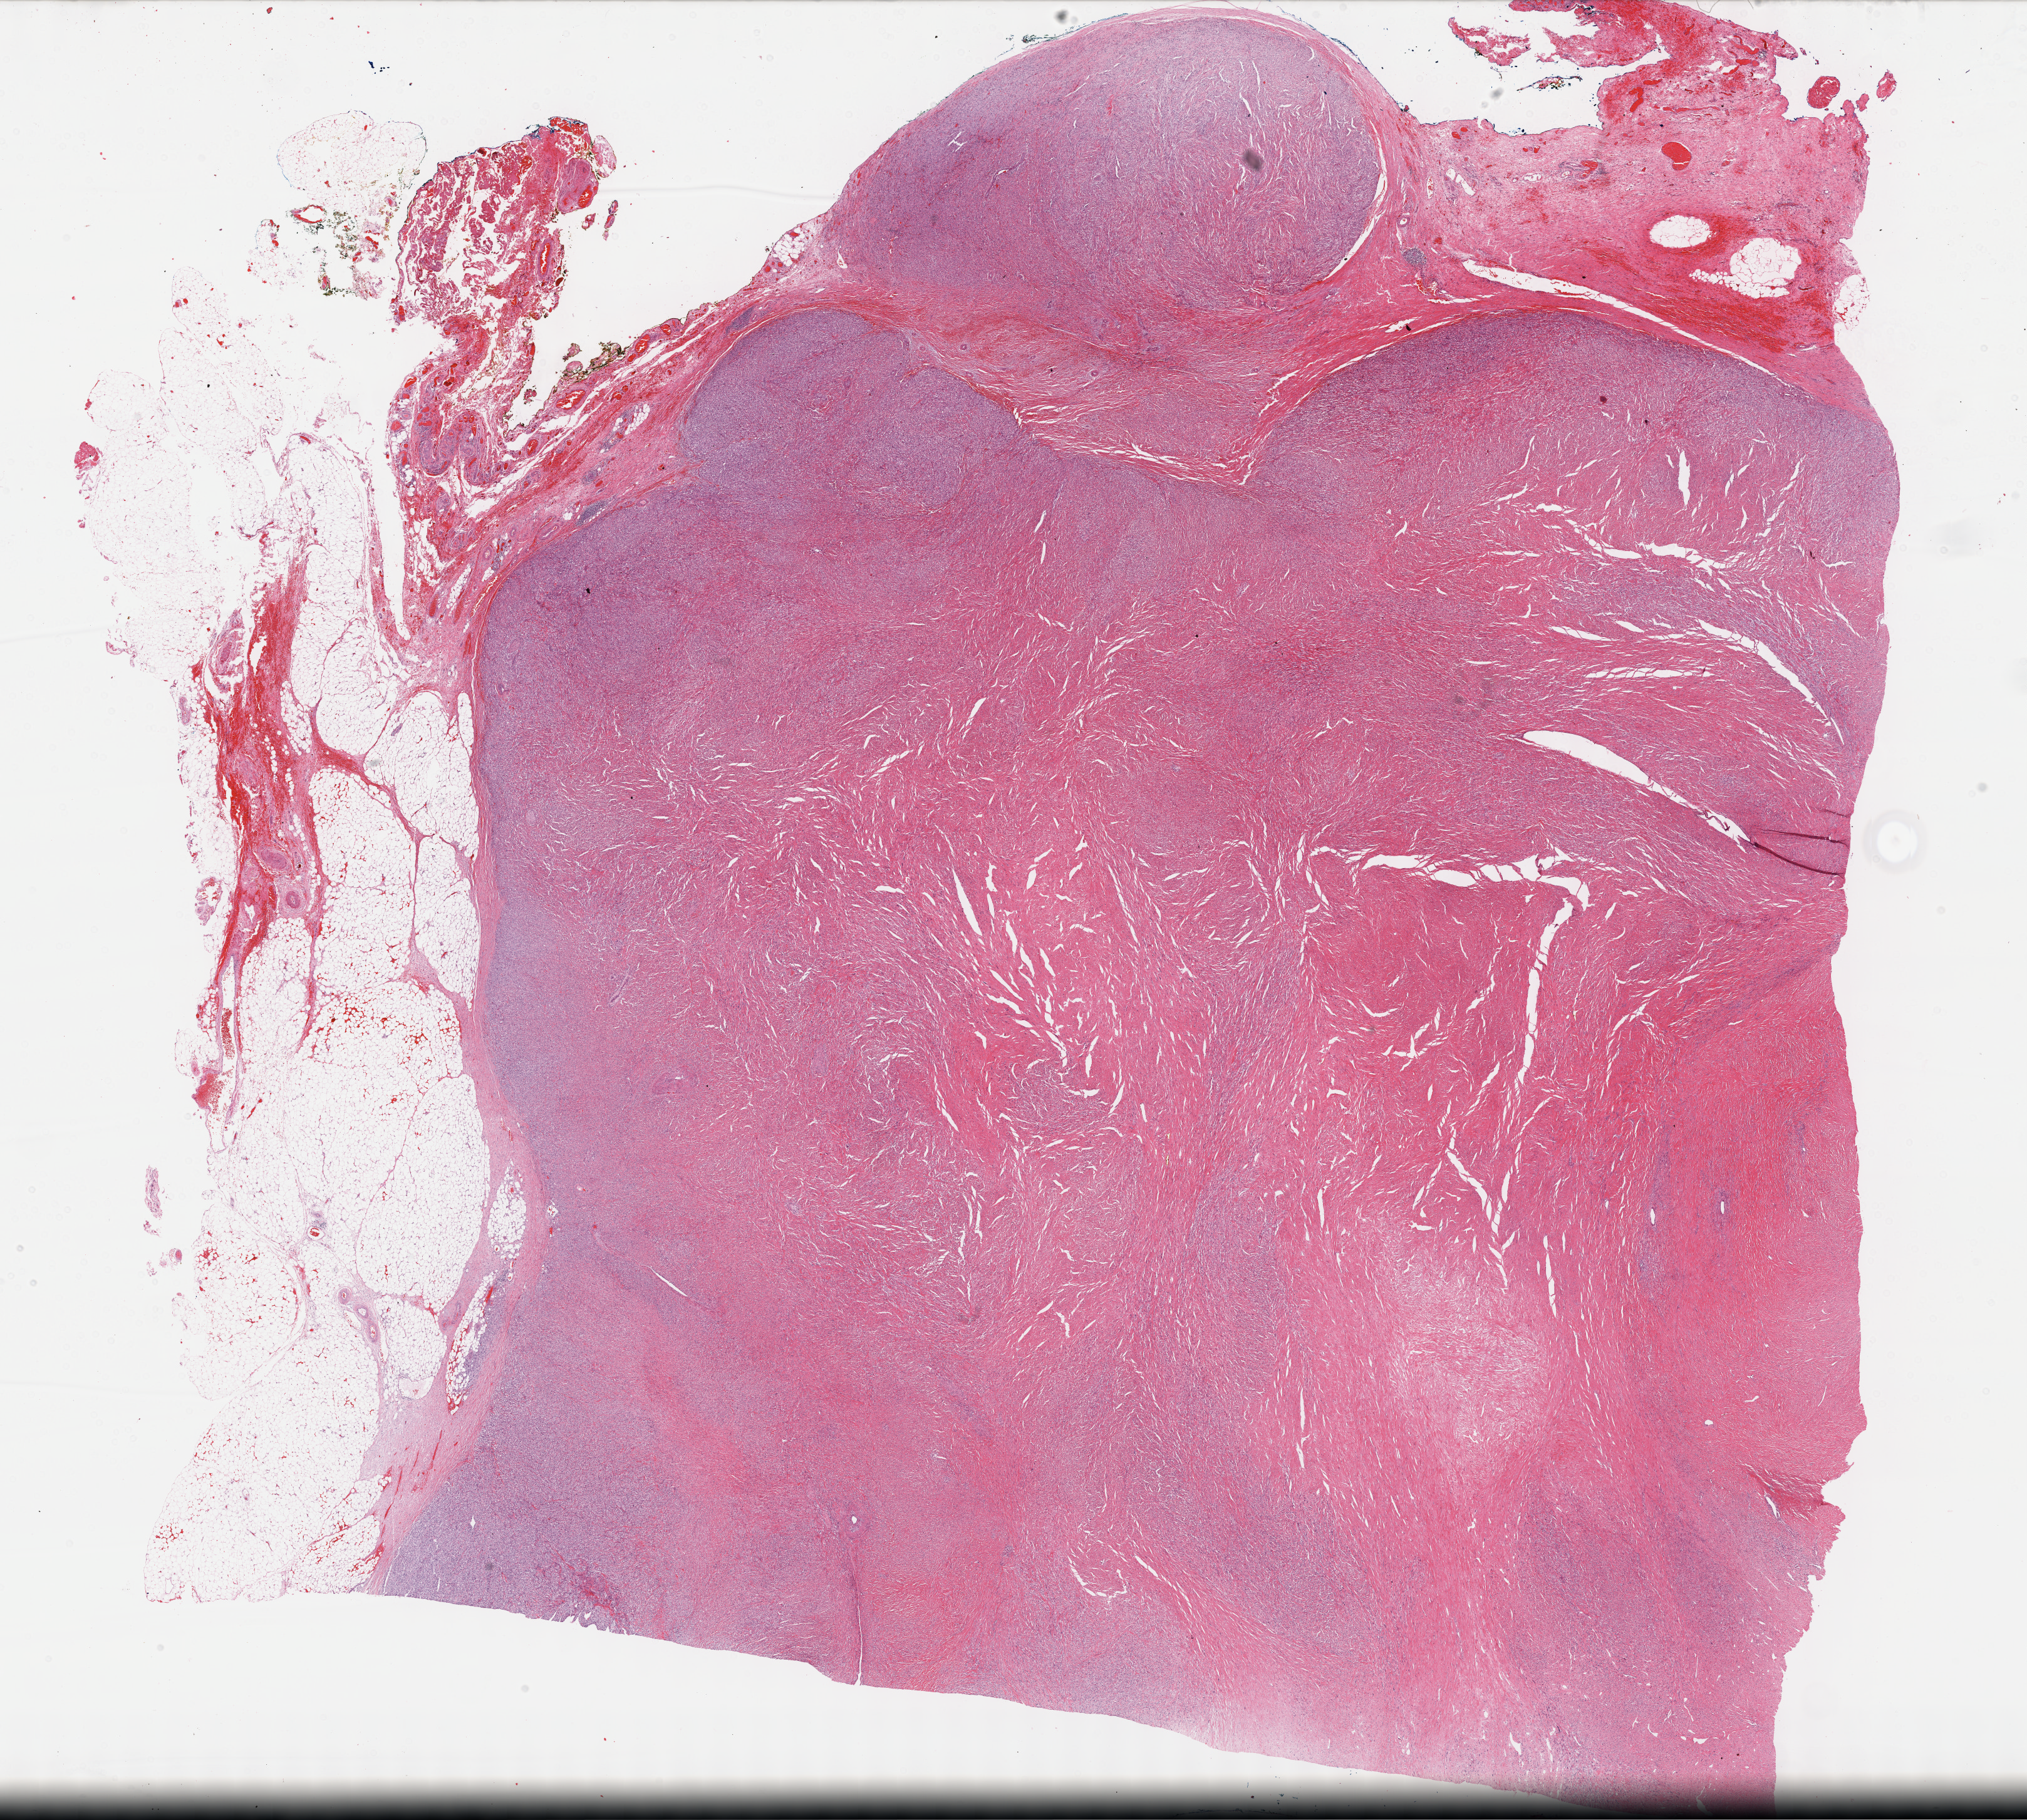
H&E whole-slide image — low-resolution overview of the scanned area, about 26.2 x 23.5 mm (from a 40x scan); formalin-fixed paraffin-embedded (FFPE) diagnostic section; primary tumour sample from the retroperitoneum and peritoneum. Female patient; age at initial diagnosis 66 years.
Diagnosis: Dedifferentiated liposarcoma.